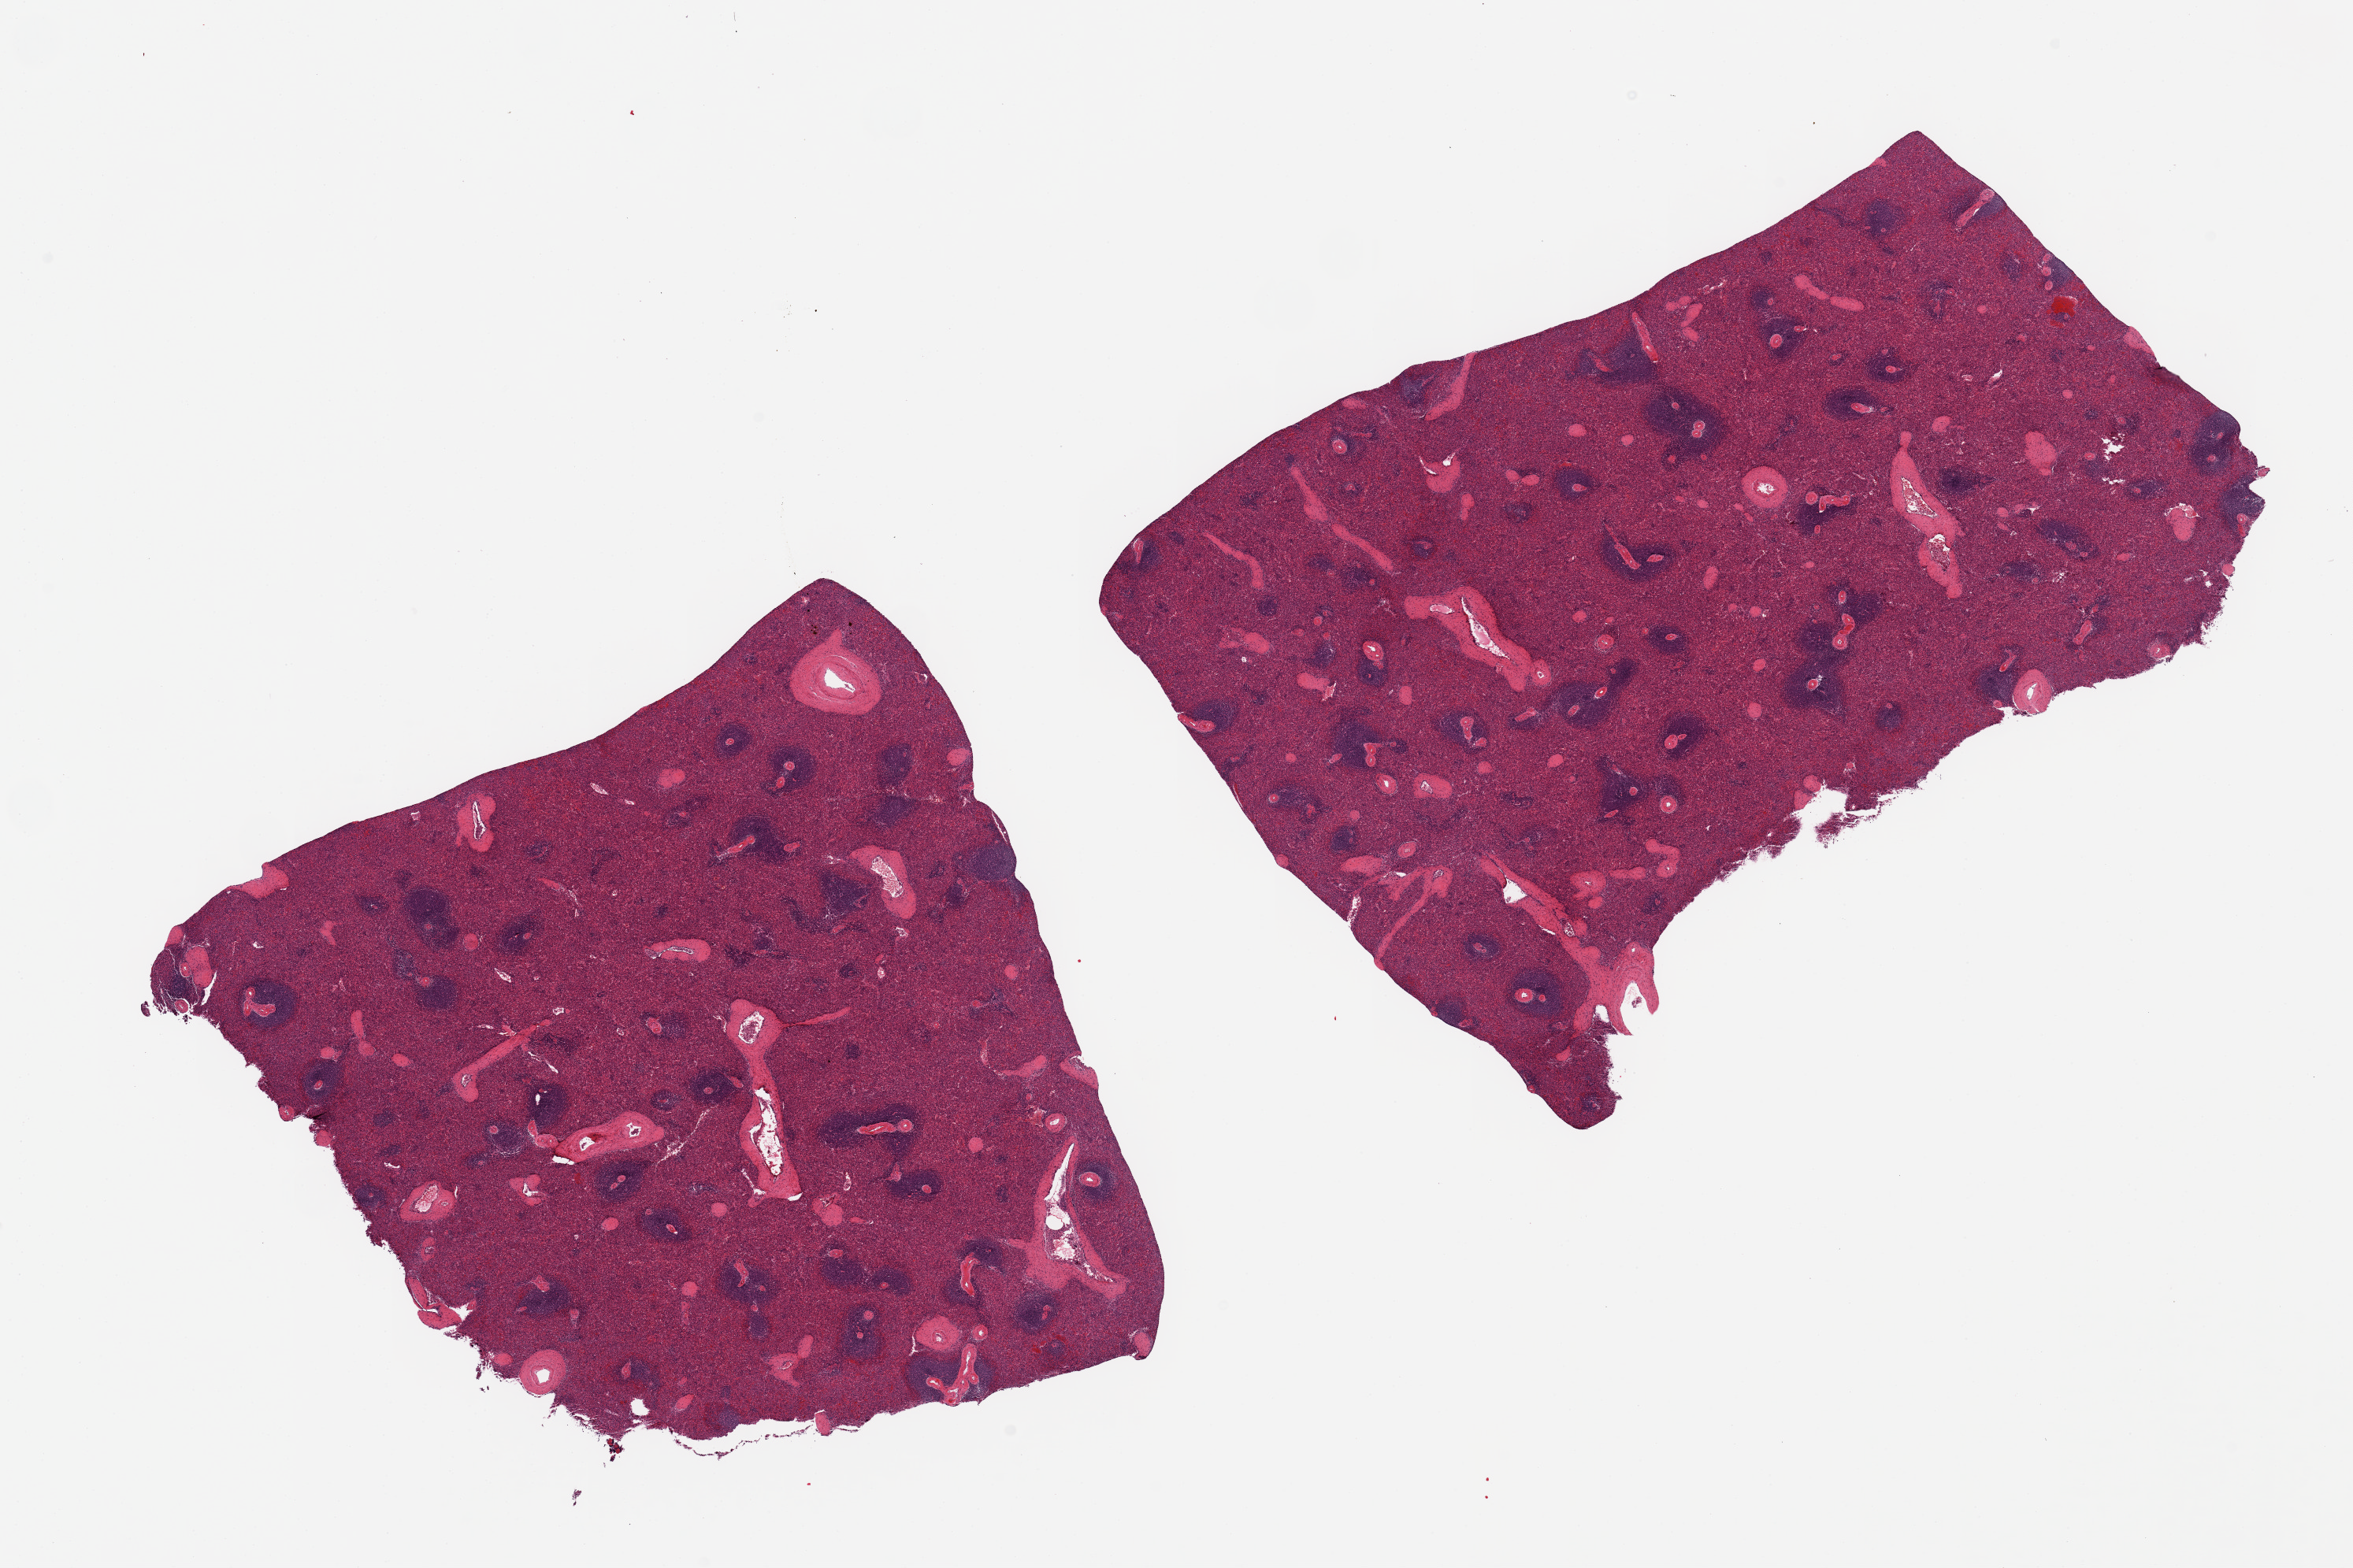
Digitized haematoxylin and eosin-stained section, a low-resolution overview of the entire scanned area, about 23.6 x 15.7 mm, PAXgene-fixed paraffin-embedded (PFPE) section, section of spleen (target tissue), donor tissue sample. Female donor.
* pathologist's review note for this sample: 2 pieces, mild congestion